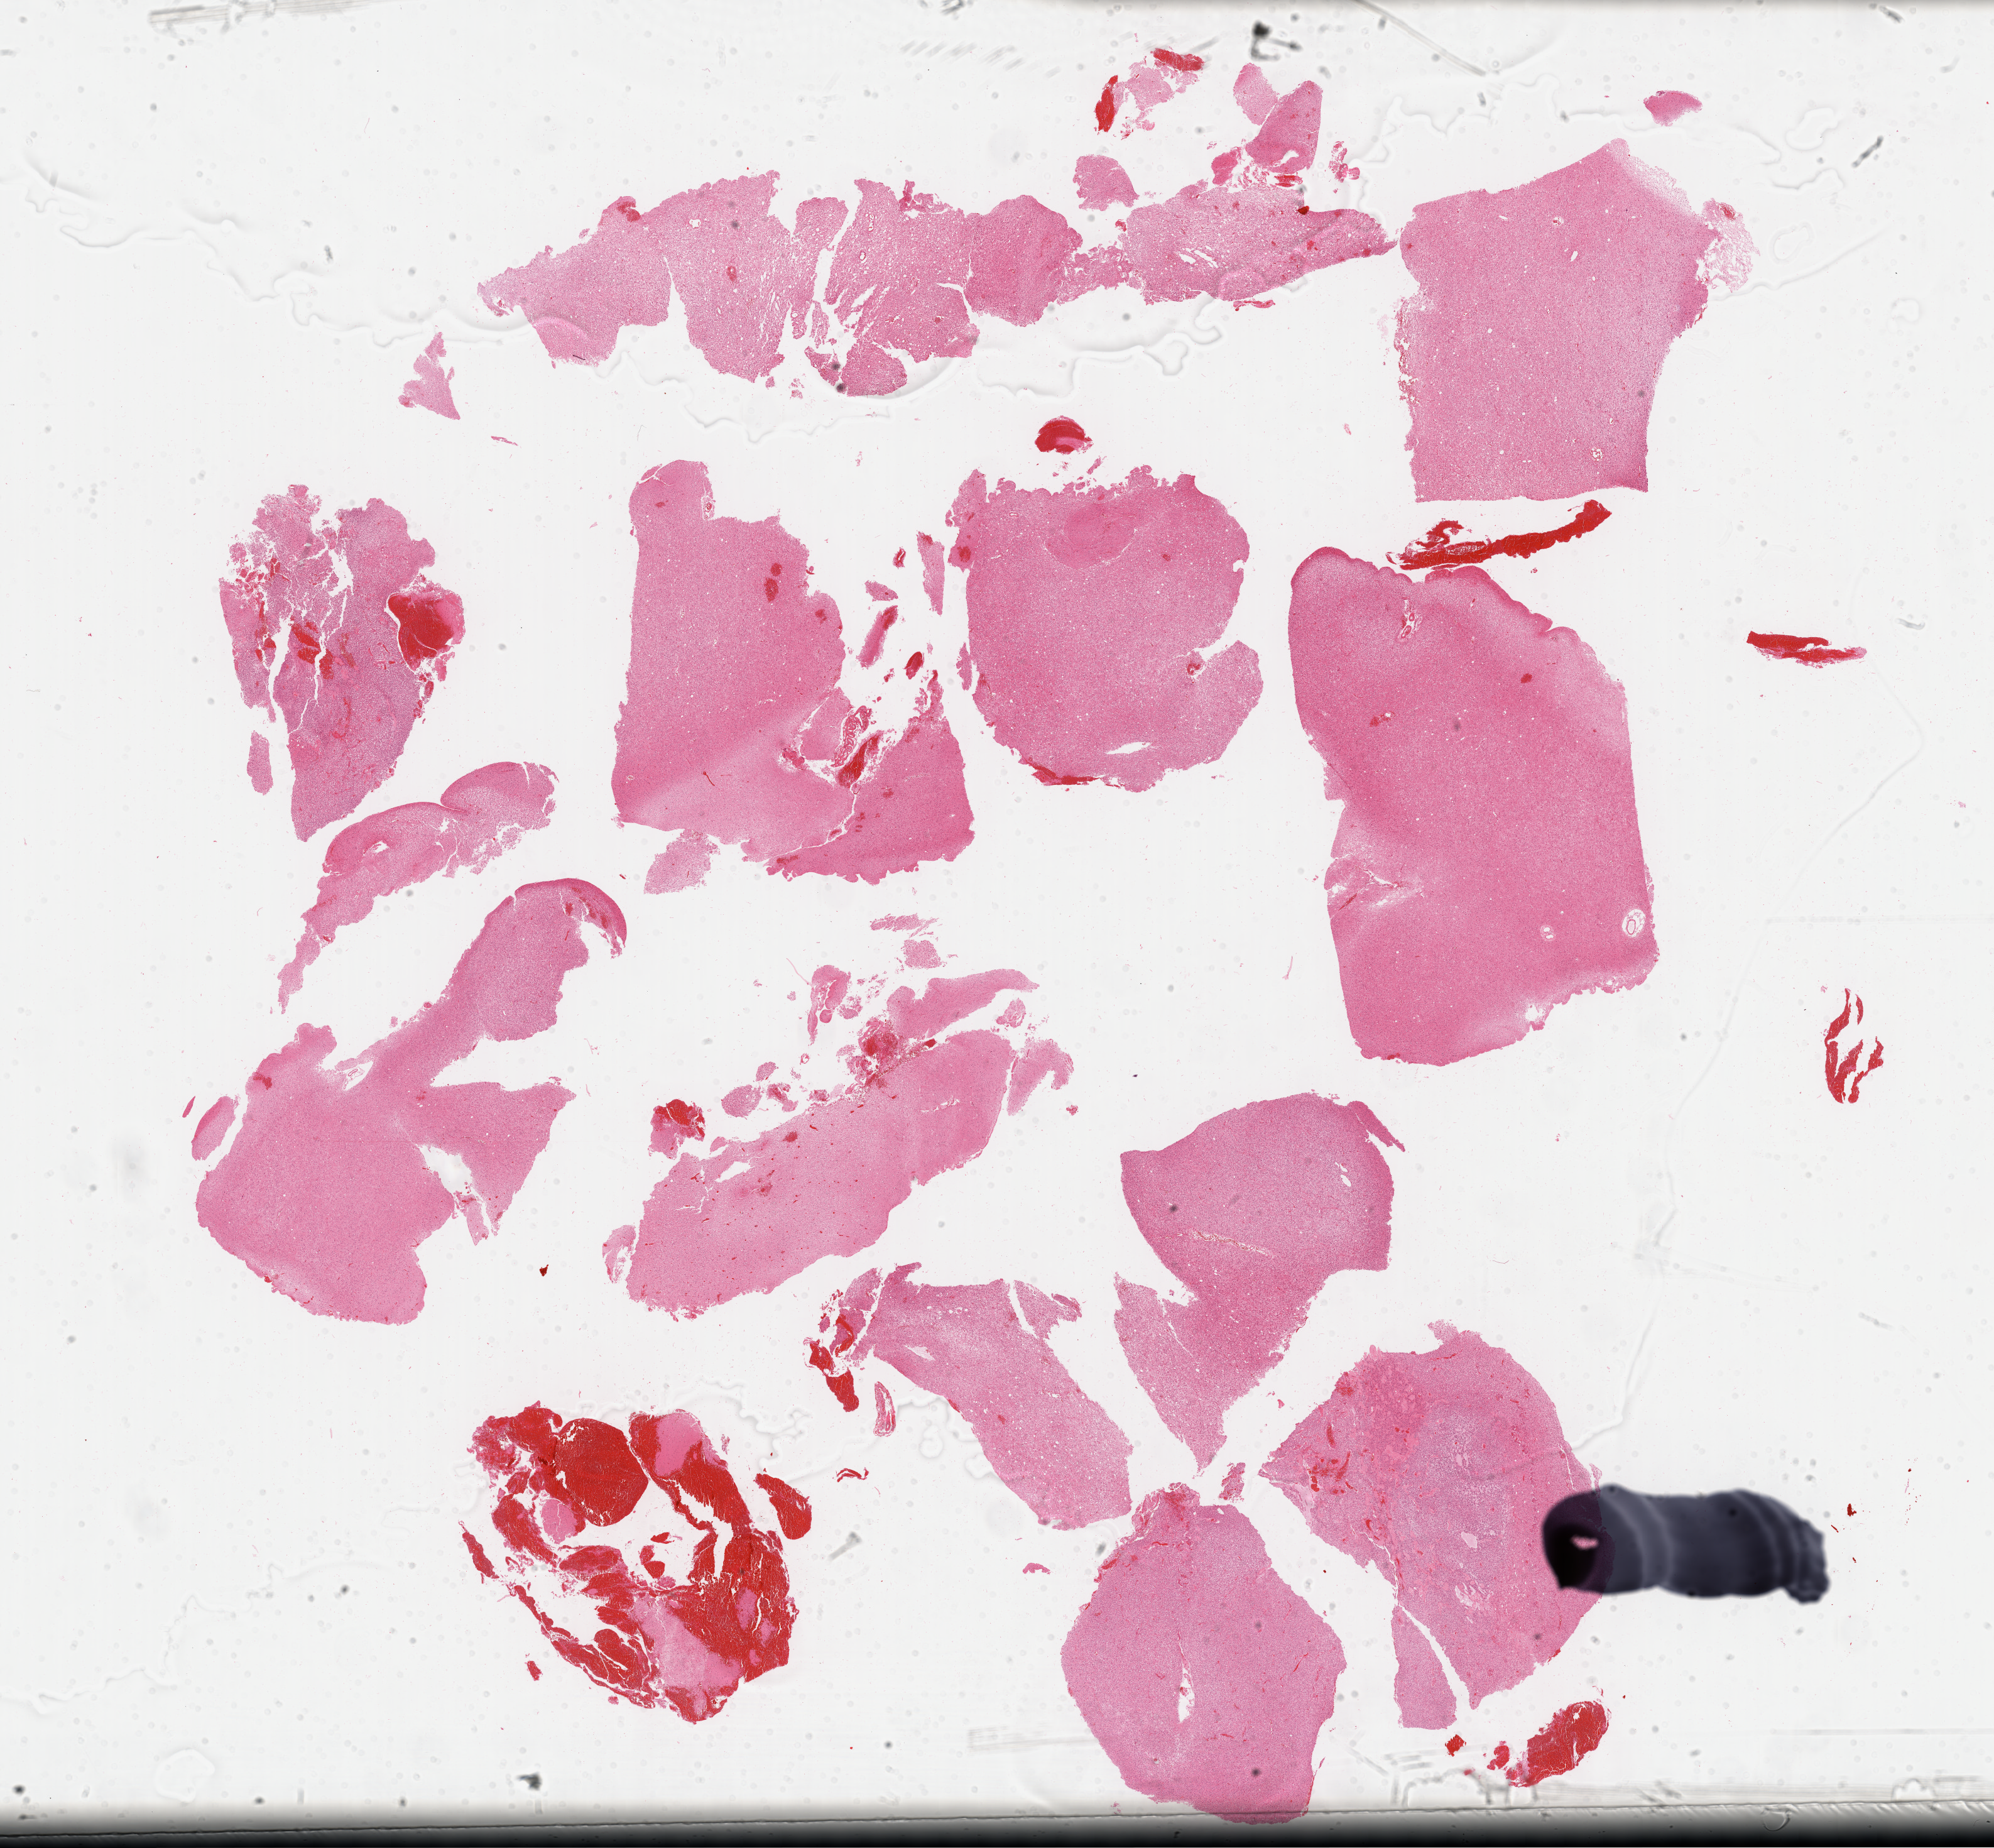
H&E whole-slide image — whole scanned area (about 25.7 x 23.8 mm) shown as a low-resolution overview, FFPE section, brain, primary tumour sample. Patient: male, age at initial diagnosis 25 years. Histologic grade: G3 (poorly differentiated).
Histologic diagnosis: Oligodendroglioma, anaplastic. Laterality: left.